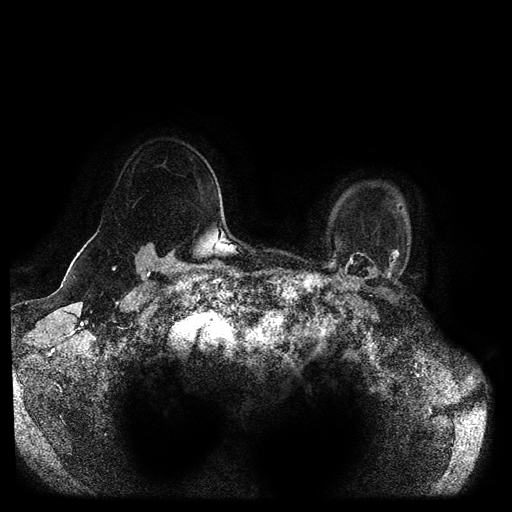
Breast MRI (dynamic contrast-enhanced, multi-phase), one axial slice. Dynamic contrast-enhanced series, time point 2 of 5 at this slice position (early post-contrast). 1.5 T. TE 2.6 ms, TR 5.3 ms. 2 mm slice thickness. 512 × 512 image matrix, field of view 370 × 370 mm. Female patient, age 55 years.
Structures marked on this image (semi-automatic segmentation, software-assisted and operator-edited):
- breast lesion (labelled benign in the annotation): box from (x=341, y=248) to (x=400, y=285) px